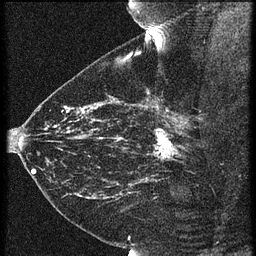
Breast MRI (dynamic contrast-enhanced), one sagittal slice. Slice 41 of 60 in the series (ordered by position). 3 images stored at this slice position (order not interpretable as contrast timing). 1.5 T. TE 4.2 ms, TR 21.3 ms. 1.5 mm slice thickness. 256 × 256 image matrix, field of view 180 × 180 mm. Female patient, age 43 years. From the clinical record (not read from this slice): setting: breast cancer imaged before/during neoadjuvant chemotherapy; receptor status: HER2-positive.
Annotated regions visible in this slice (semi-automatically segmented with operator editing):
- analysis volume of interest (the breast-tissue region the enhancement analysis was run in; not a lesion): bounding box <119,114,189,173> (left, top, right, bottom; pixels)
- tumour enhancement mask (voxels above the 90 % enhancement threshold inside the analysis volume of interest): <154,116,177,161>